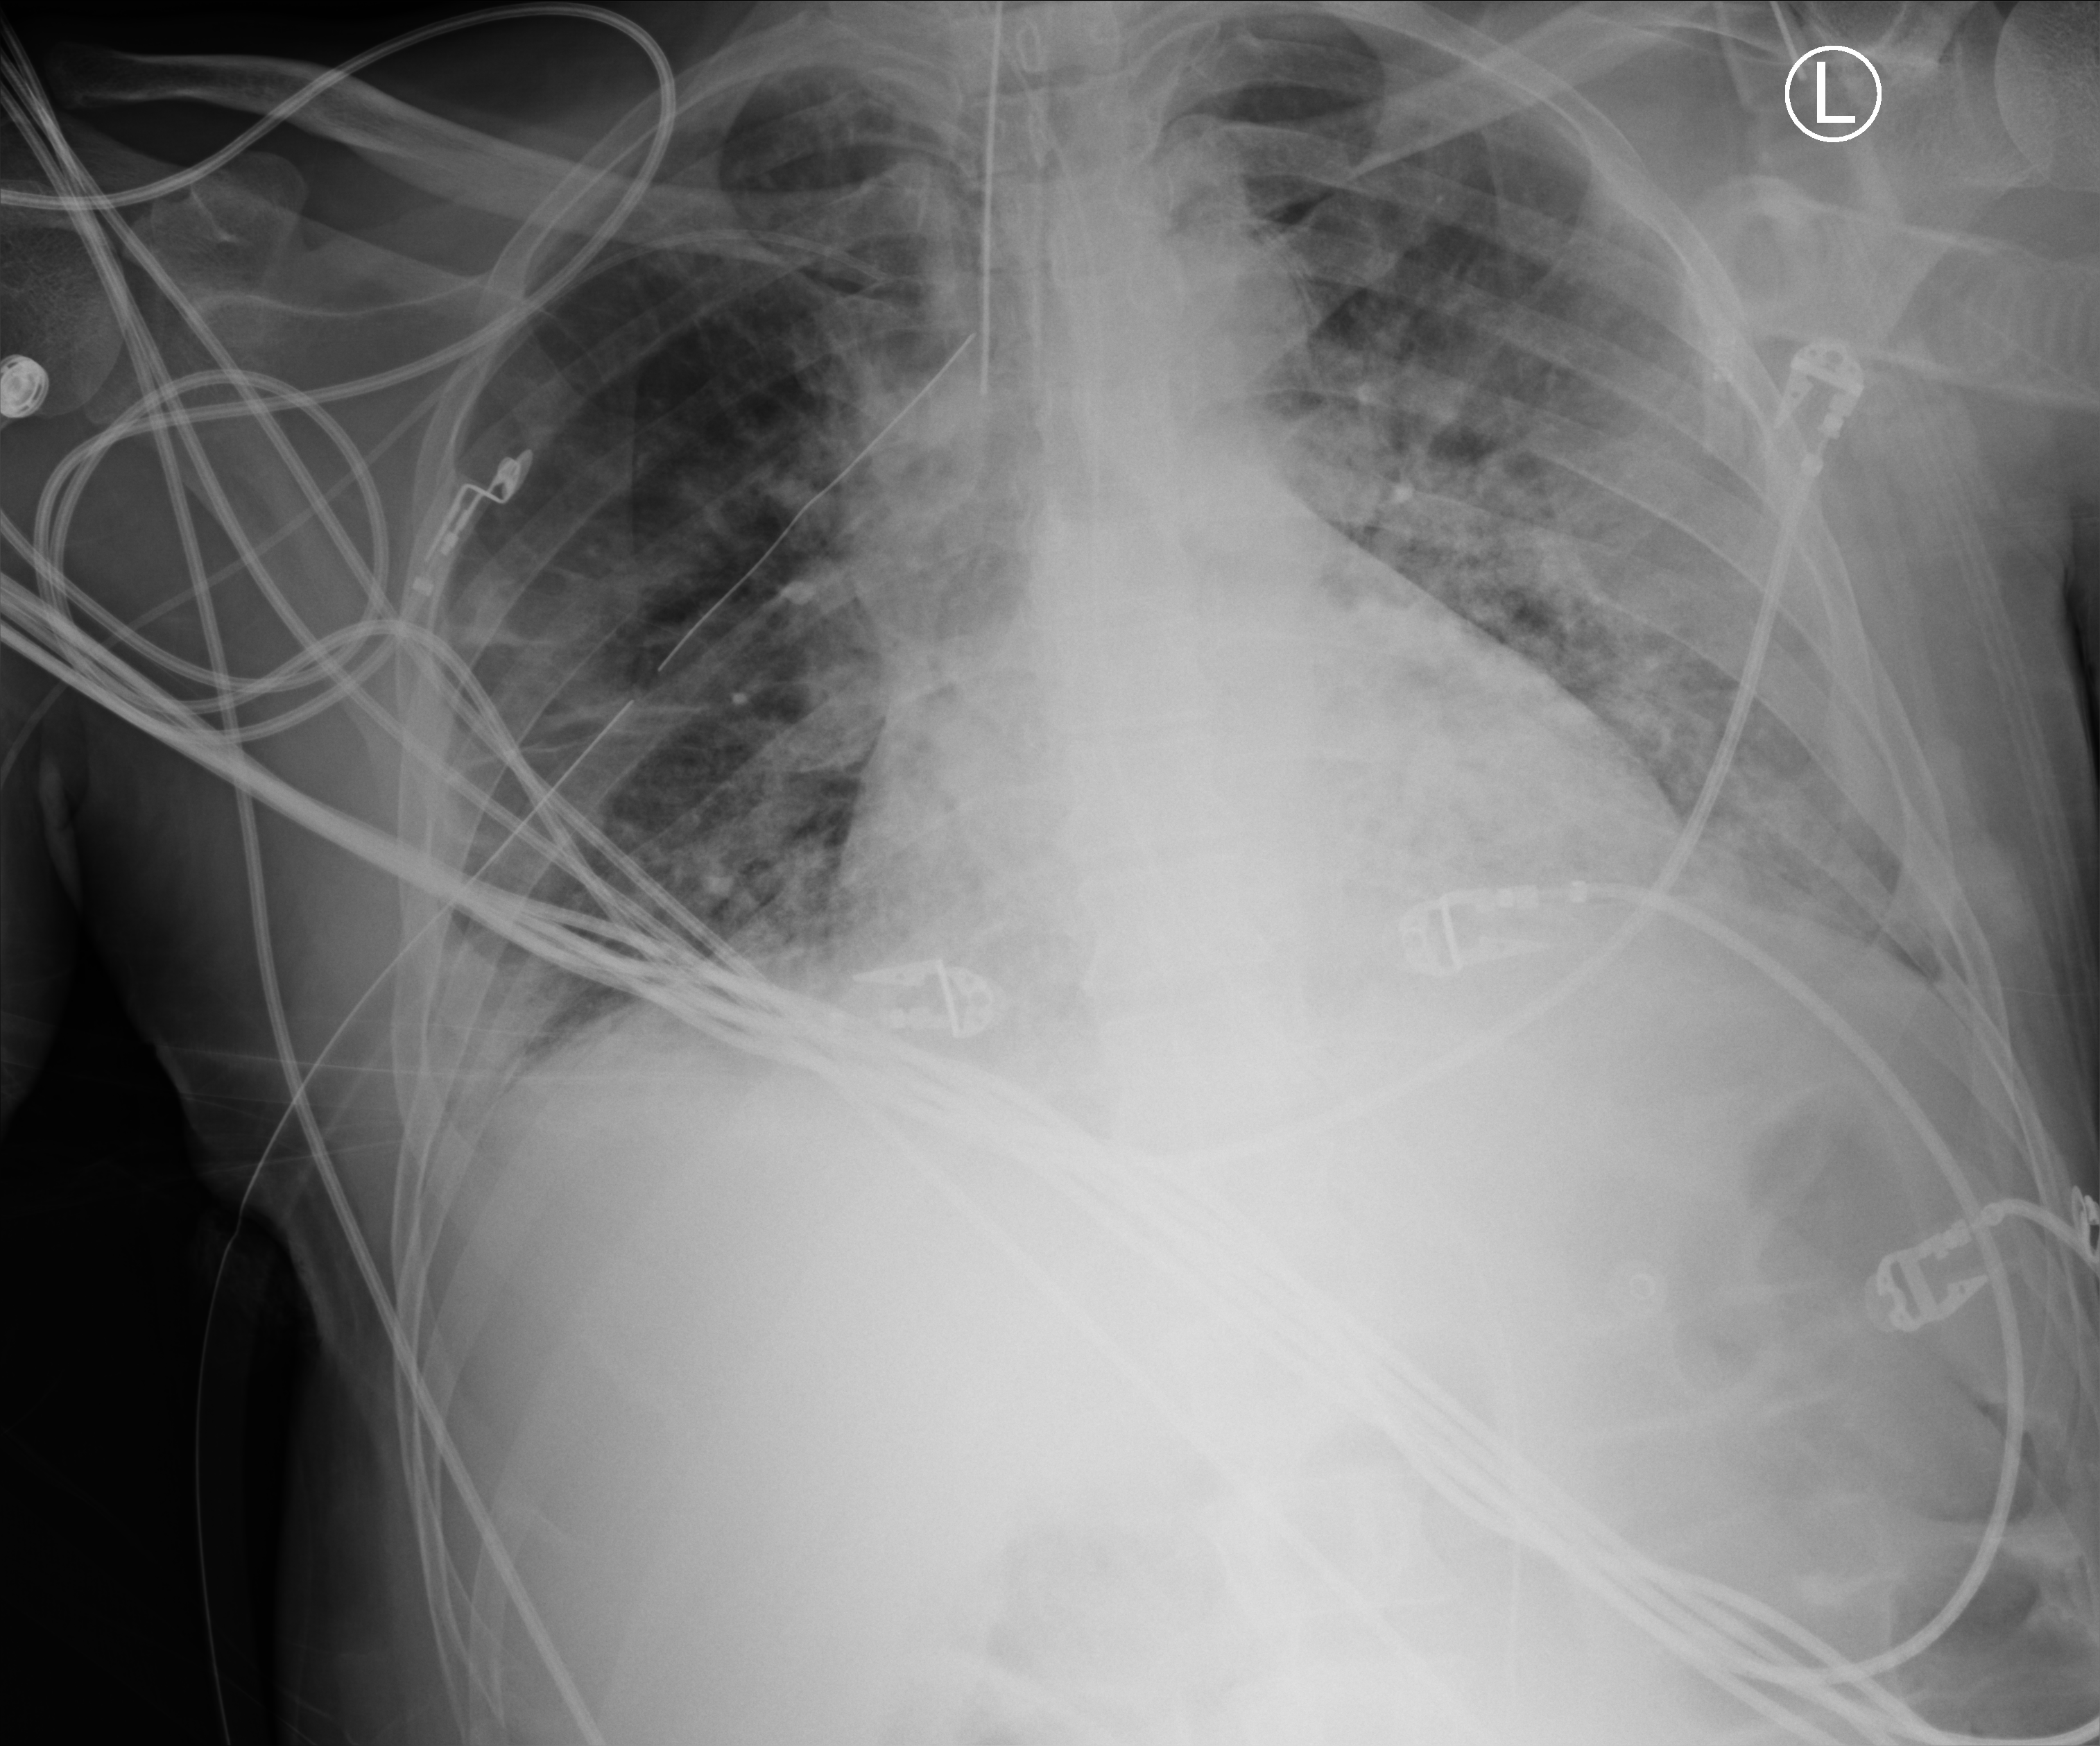
Chest X-ray (portable). Male patient hospitalised with COVID-19, age 18–59 years.
Hospital-stay facts (about this admission, not read from this image; timing relative to this image not recorded): admitted to intensive care during this hospital stay: yes.